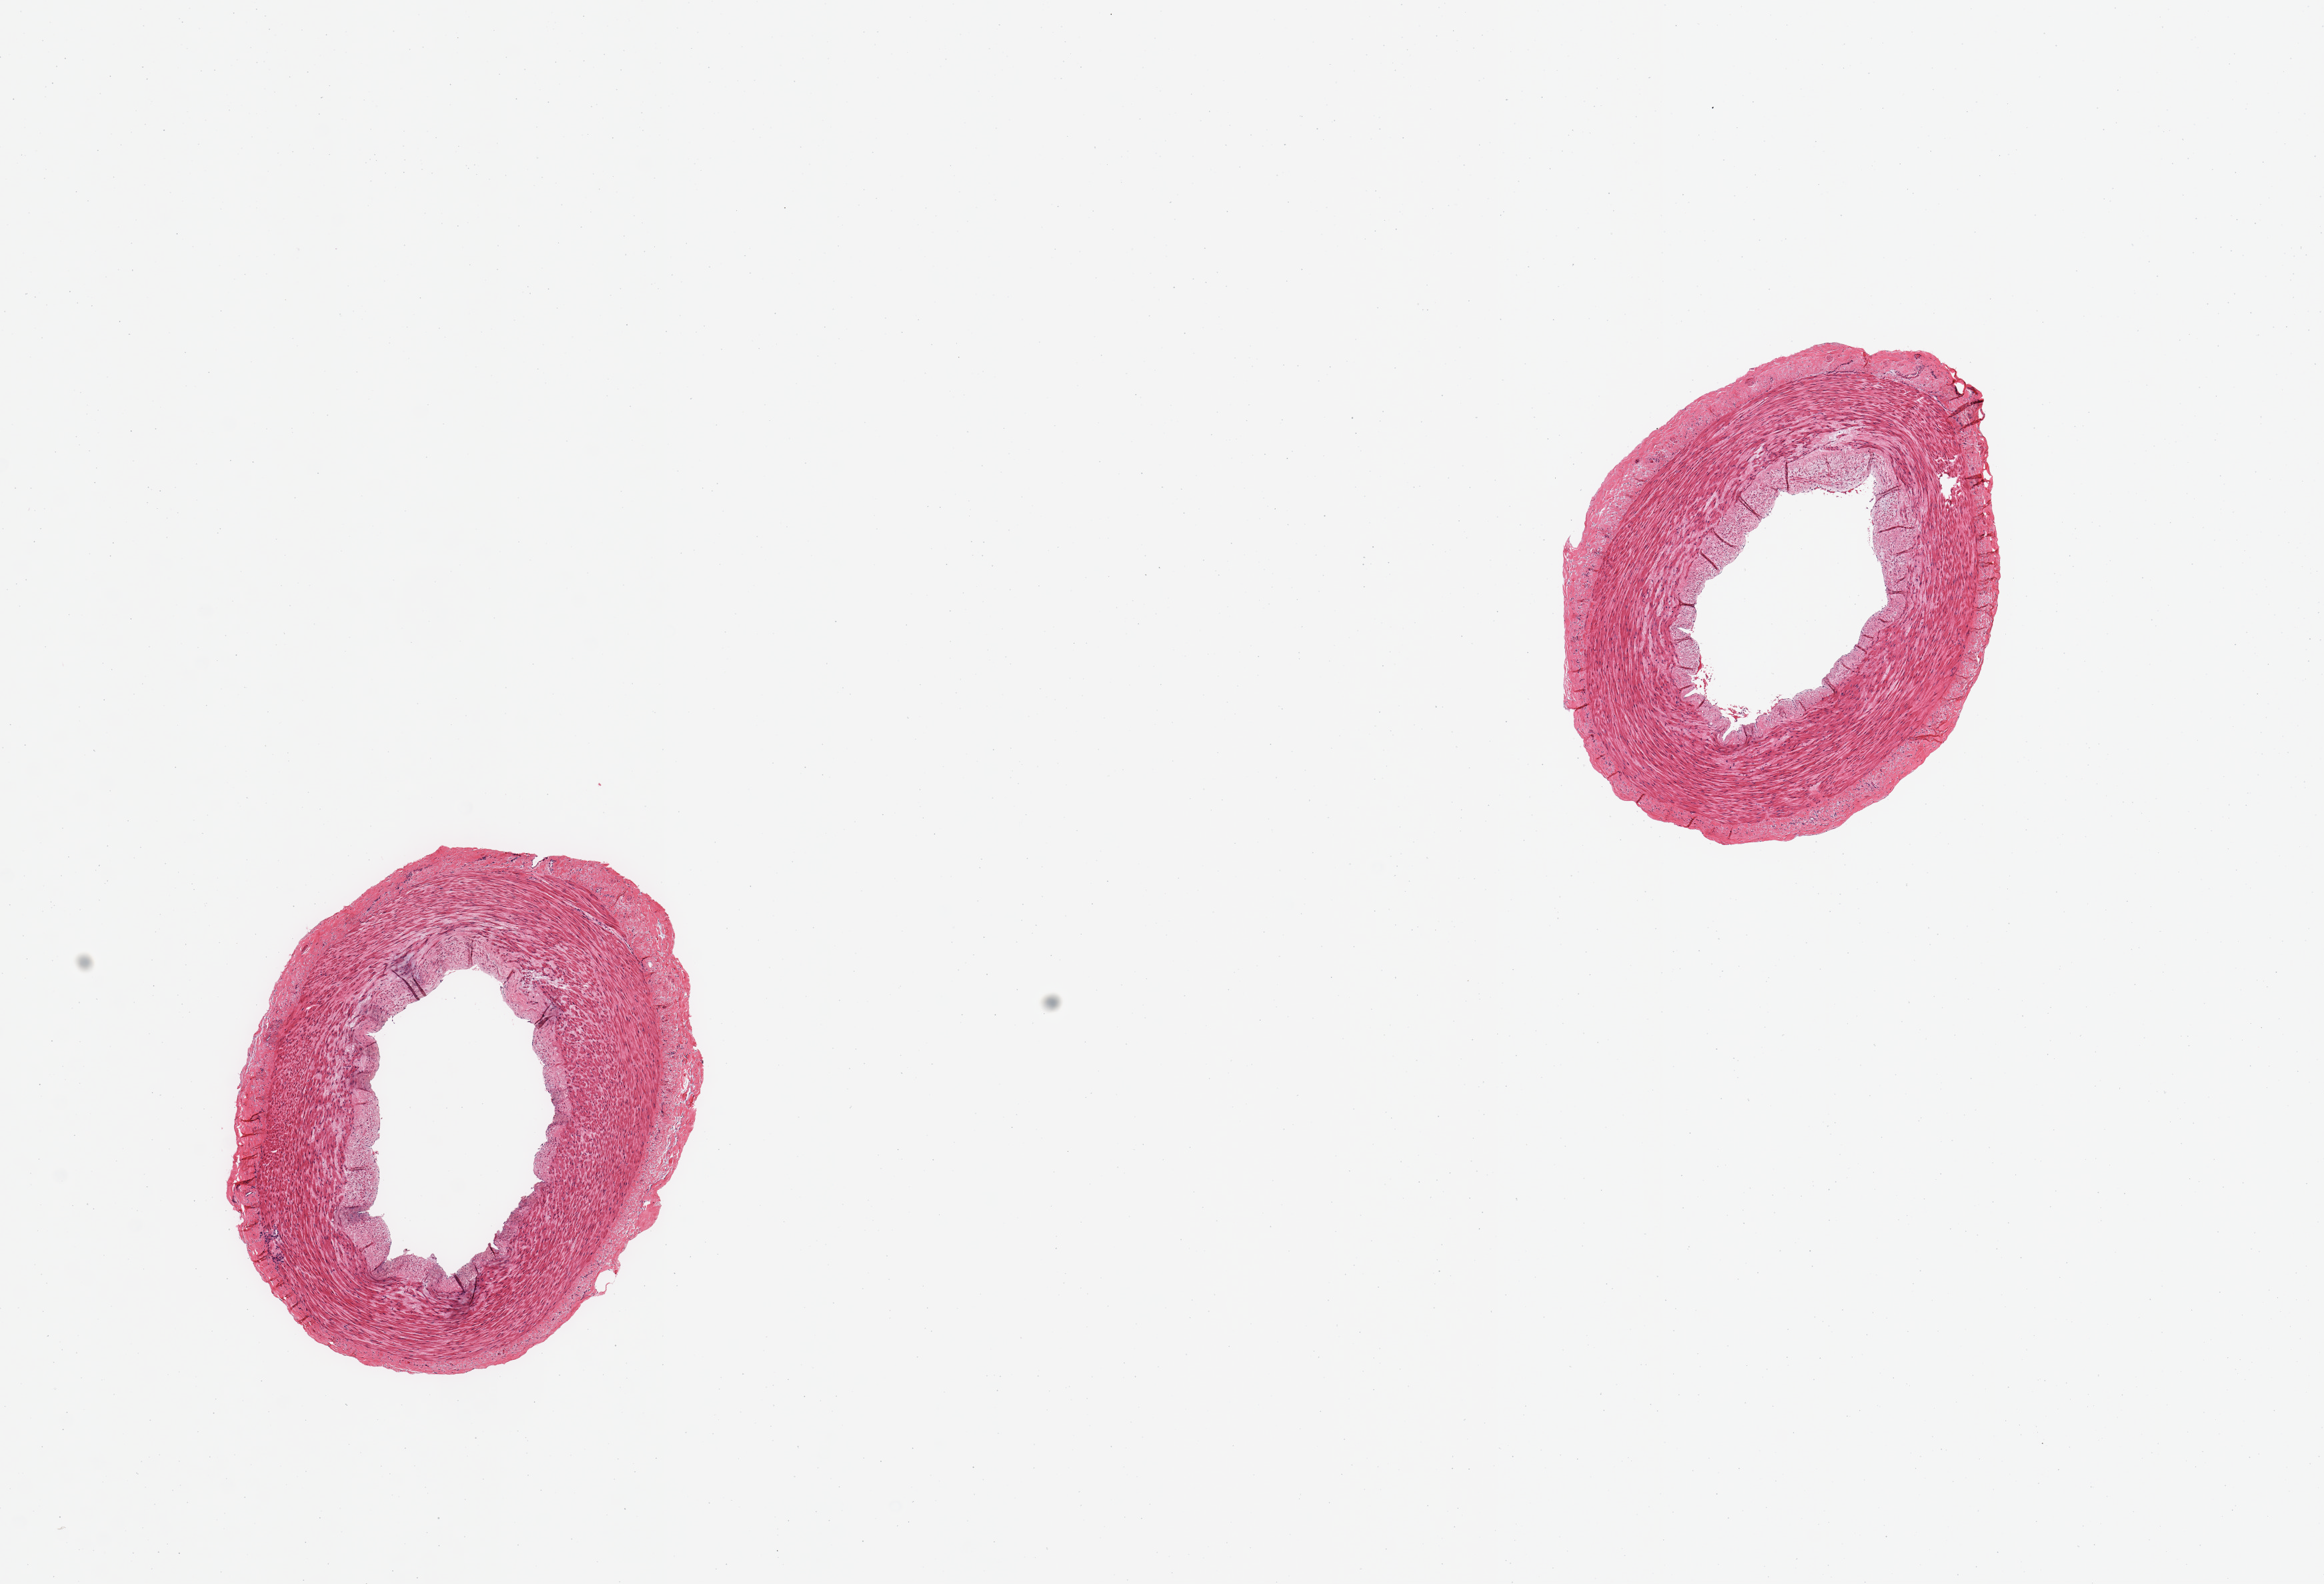
Whole-slide image, haematoxylin and eosin stain, brightfield — a low-resolution overview of the entire scanned area, about 13.8 x 9.4 mm (from a 20x scan), PAXgene-fixed, paraffin-embedded tissue, section of tibial artery (target tissue), donor tissue sample. Donor sex: male.
Reviewer comment on this tissue sample: 2 pieces, no significant adherant fat.